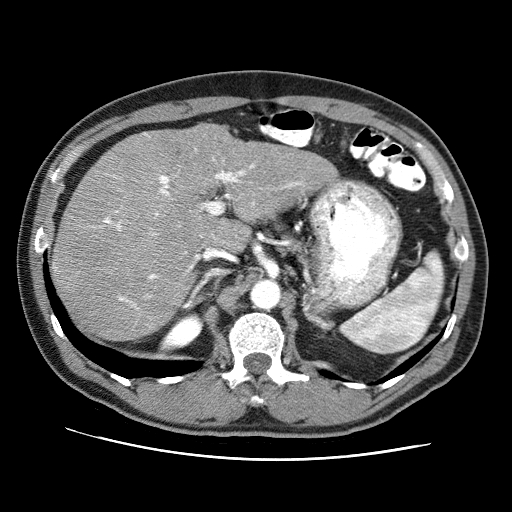
Contrast-enhanced abdominal CT (liver protocol), one axial slice; position 48 of 71 along the scan axis; reconstruction kernel STANDARD; 120 kVp; soft-tissue window (W 400 / L 40 HU); 512 × 512 image matrix. Case-level facts recorded for this patient, not image findings: diagnosis: hepatocellular carcinoma (patient treated with transarterial chemoembolisation; whether this scan precedes or follows treatment is not stated here); TNM stage (as recorded): Stage-II; Child-Pugh class: A; tumour differentiation: well differentiated; tumour nodularity: multinodular.
Structures marked on this image (semi-automatically segmented with operator editing):
- abdominal aorta: bounding box <252,281,279,308> (left, top, right, bottom; pixels)
- liver parenchyma outside the tumour (the mass and vessels are separate outlines, so this box may not span the whole liver): <50,124,336,340>
- liver vessels: <104,133,300,301>